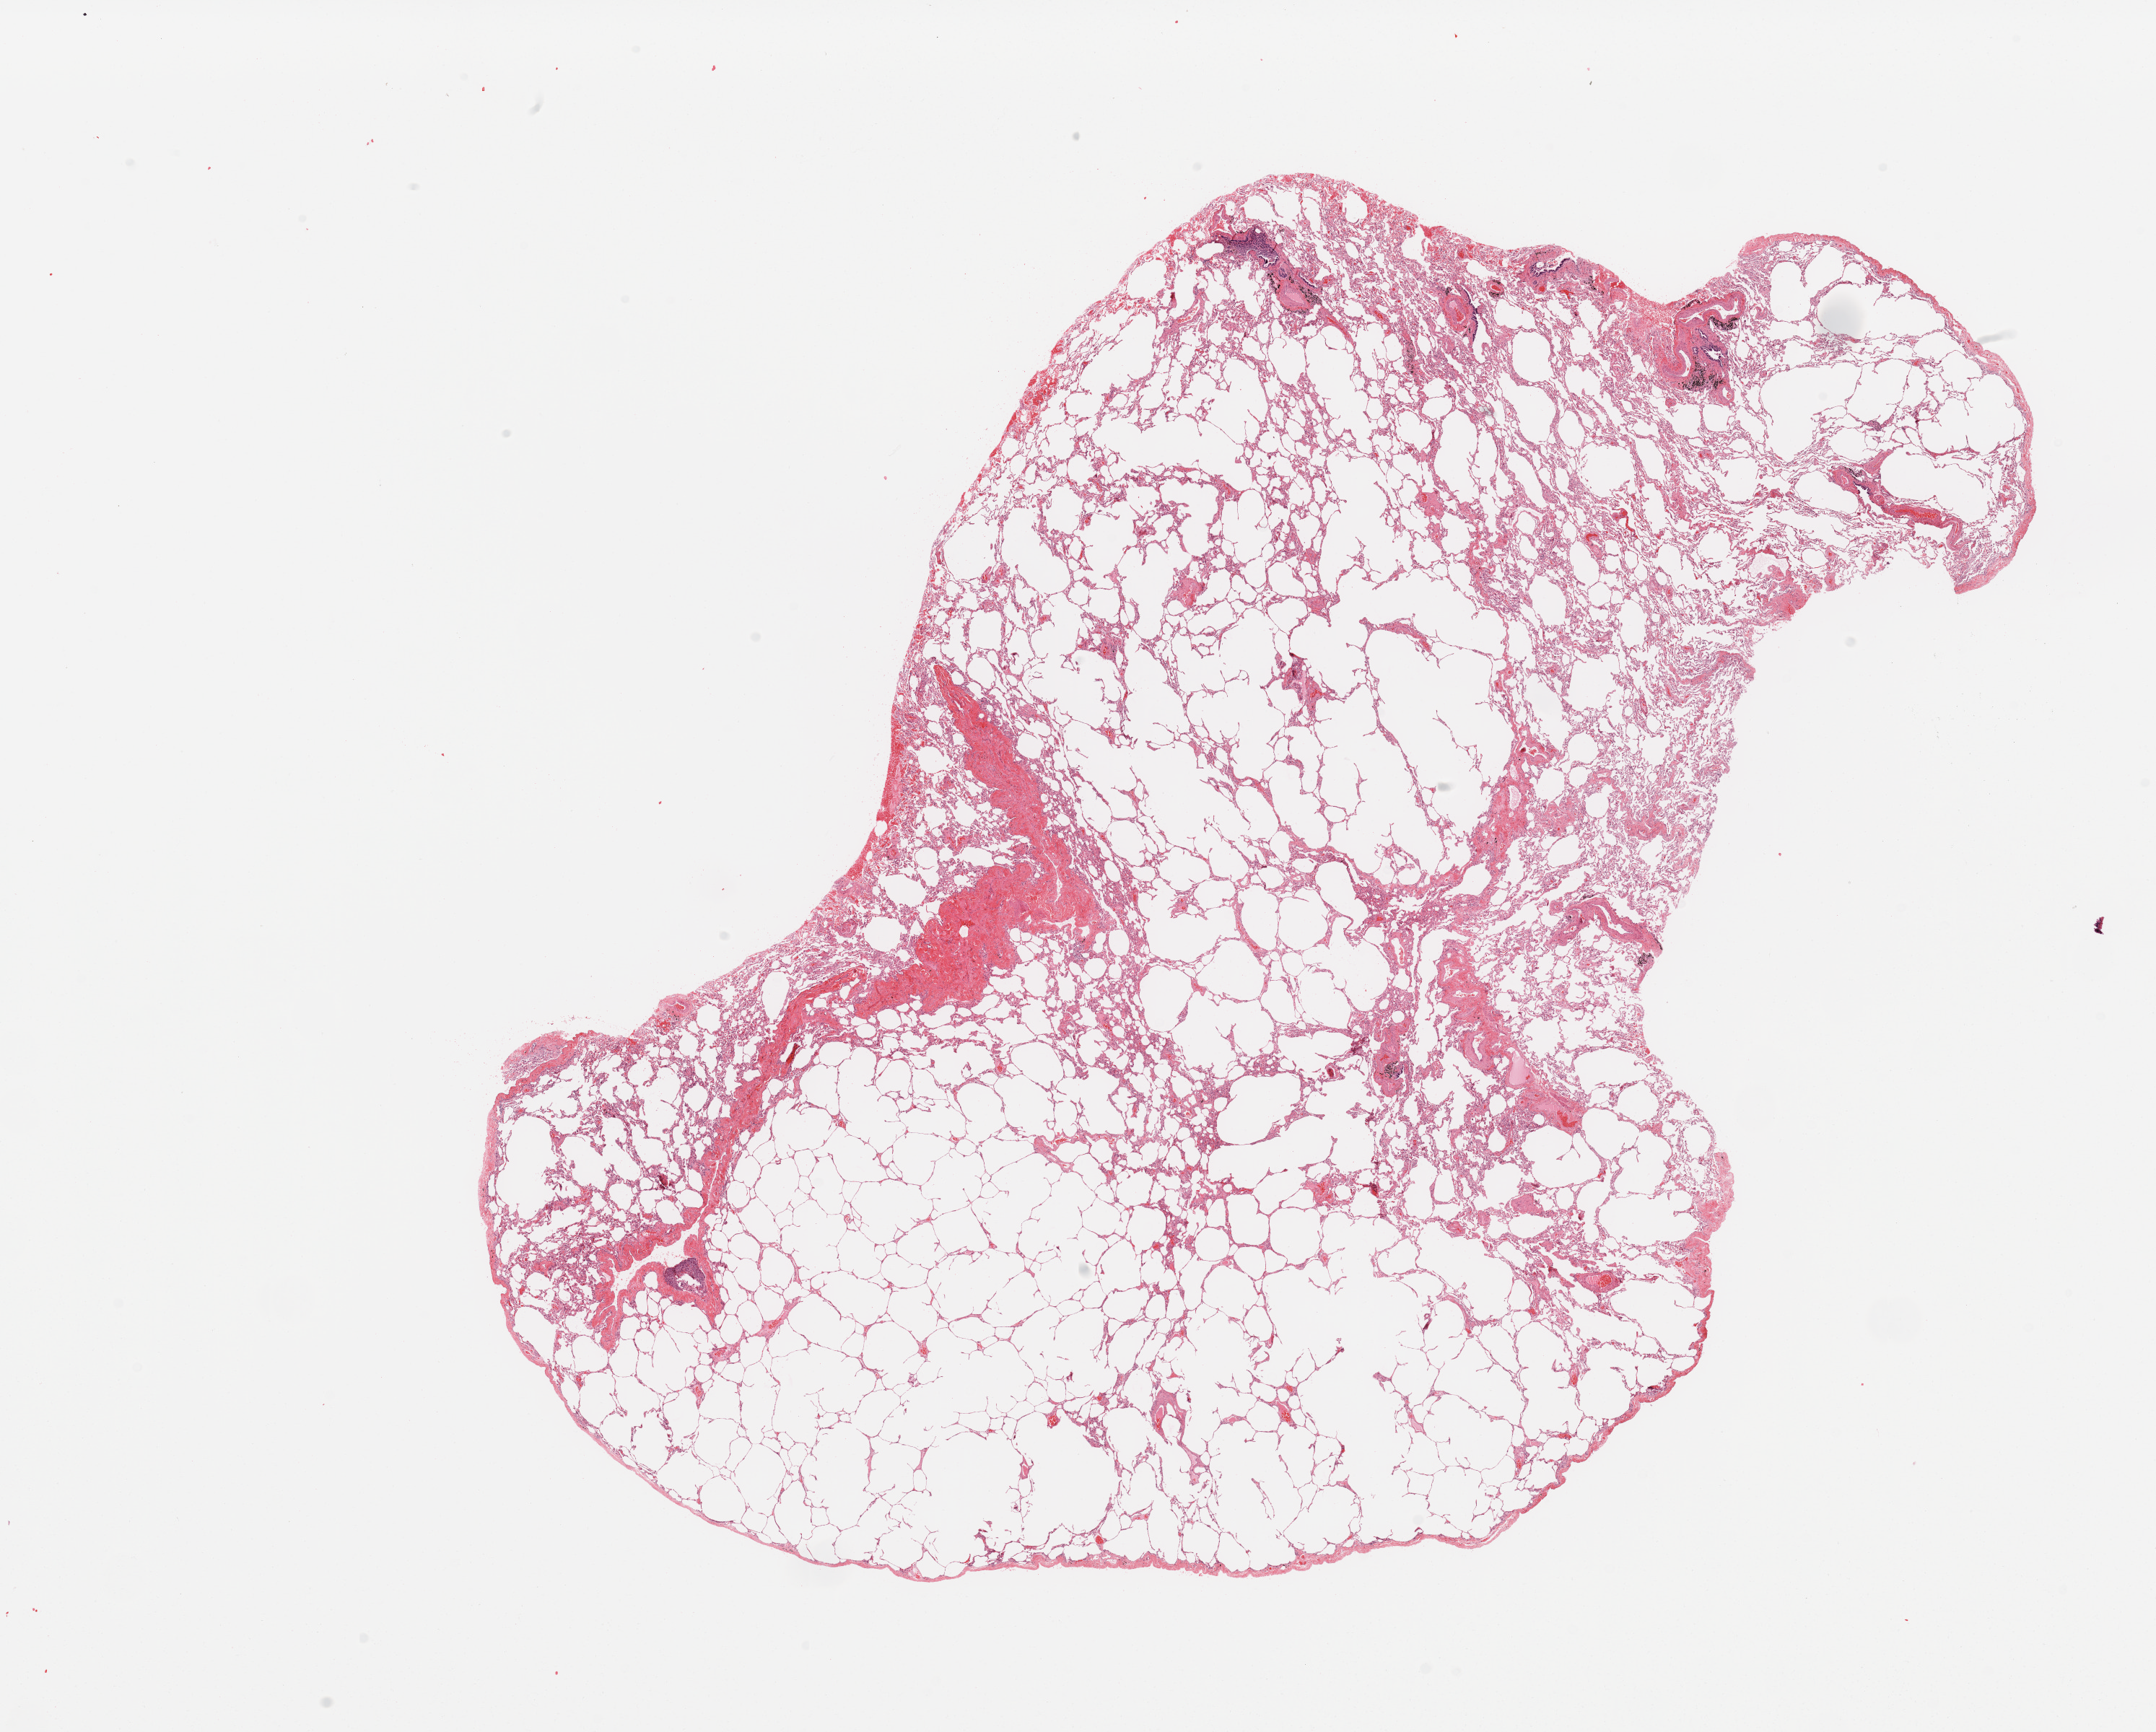
Digitized Hematoxylin and eosin (H&E) stained tissue section (whole slide) — whole scanned area (about 23.6 x 19.0 mm) shown as a low-resolution overview. Normal (non-tumour) tissue sample, sampled site: lung. Male, 49 y/o.
* this section: normal (non-tumour) tissue from the same patient
* patient diagnosis: Adenocarcinoma, NOS